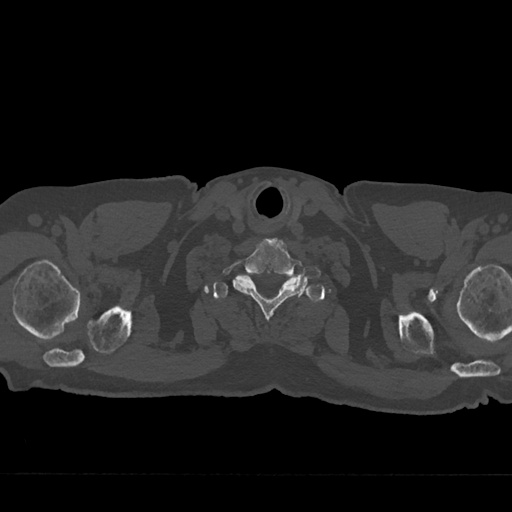
CT including the spine, one axial slice. Slice 684 of 797 in the series (ordered by position). 120 kVp. Bone window (W 1800 / L 400 HU). 0.5 mm slice thickness. 512 × 512 image matrix, field of view 377 × 377 mm. Male patient, age 75 years. Case-level facts recorded for this patient, not image findings: primary cancer: renal; vertebrae with lytic lesions (as recorded): T4.
Structures marked on this image (semi-automatically segmented with operator editing):
- T1 vertebra: bounding box <213,275,303,299> (left, top, right, bottom; pixels)